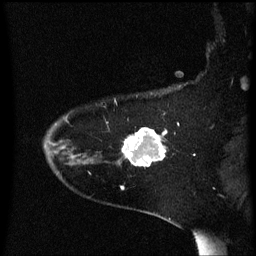
Breast MRI (dynamic contrast-enhanced), one sagittal slice; slice 47 of 60 in the series (ordered by position); dynamic contrast-enhanced series, image 2 of 3 at this slice position (ordered by acquisition); 1.5 T; TE 4.2 ms, TR 8.4 ms; 2 mm slice thickness; 256 × 256 image matrix, field of view 200 × 200 mm. Female patient, age 54 years. From the clinical record (not read from this slice): setting: breast cancer imaged before/during neoadjuvant chemotherapy; receptor status: HR-positive, HER2-negative.
Outlined on this slice (semi-automatic segmentation, software-assisted and operator-edited):
- analysis volume of interest (the breast-tissue region the enhancement analysis was run in; not a lesion): bounding box (x1, y1, x2, y2) in pixels: (119, 128, 168, 167)
- tumour enhancement mask (voxels above the 70 % enhancement threshold inside the analysis volume of interest): (123, 128, 167, 167)